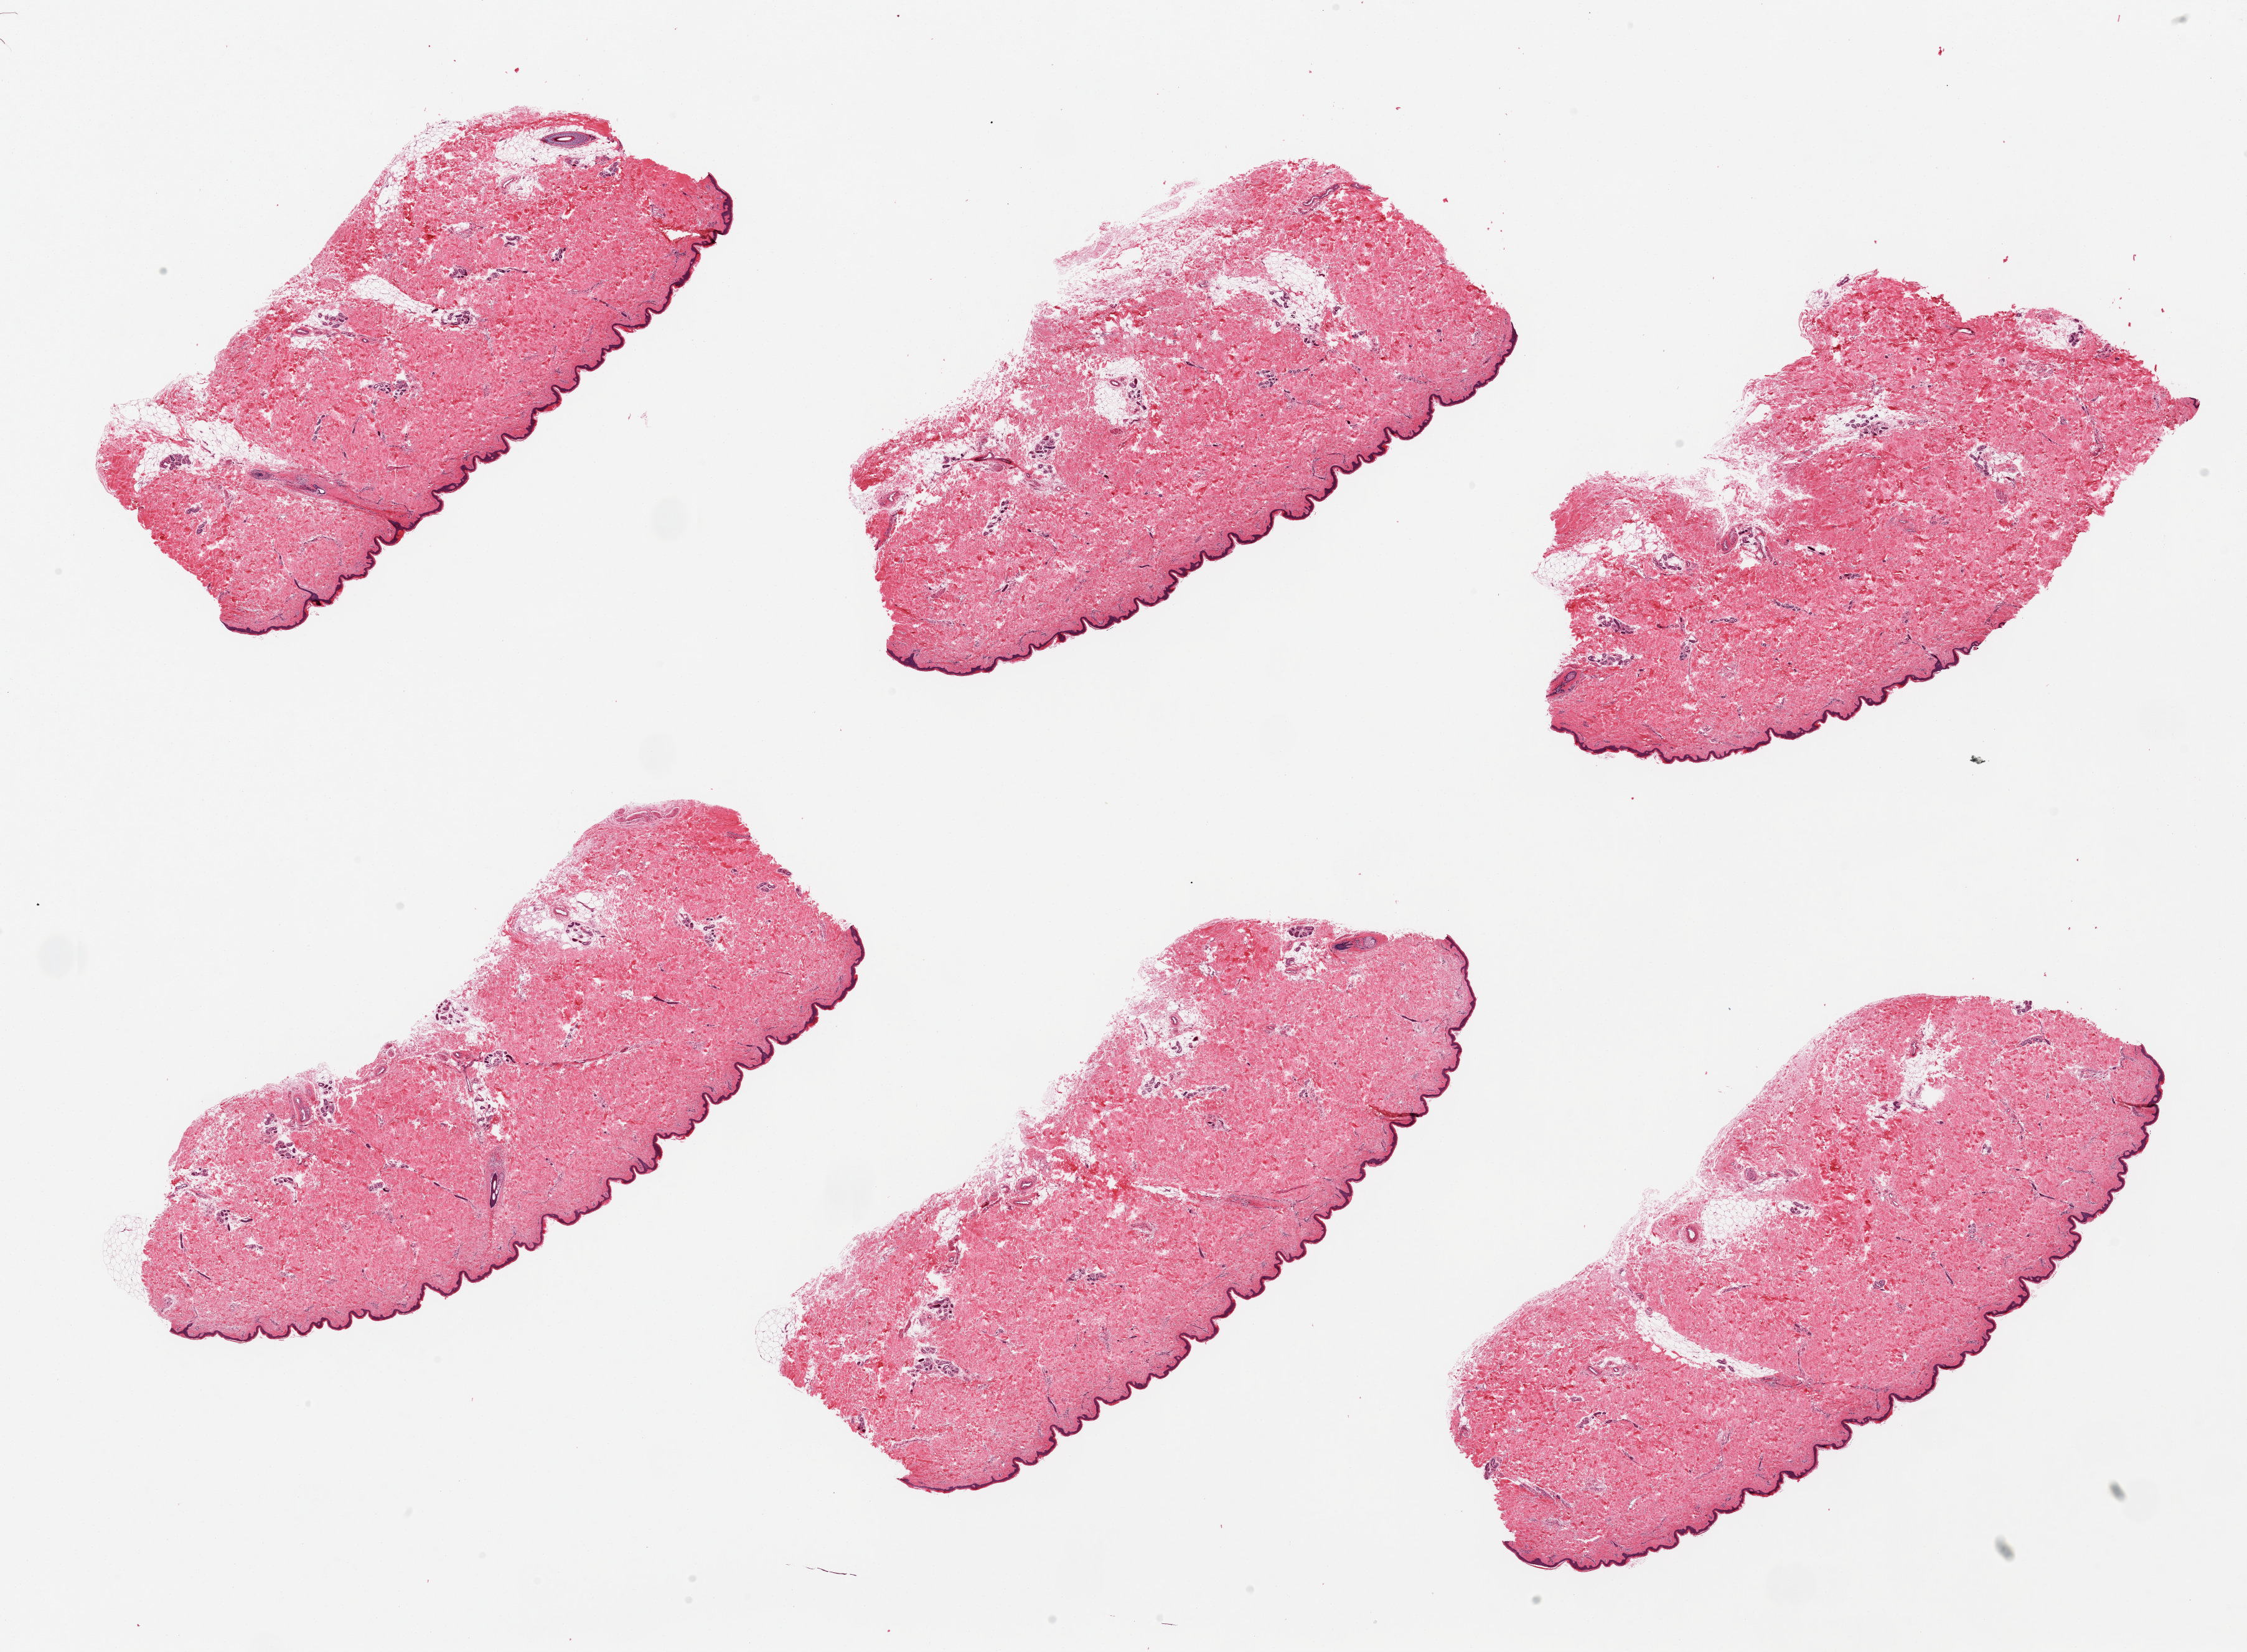
Whole-slide image, hematoxylin and eosin (H&E) stain — whole scanned area (about 28.5 x 21.0 mm, from a 20x scan) shown as a low-resolution overview, PAXgene-fixed paraffin-embedded (PFPE) section, section of skin of lower leg (target tissue), donor tissue sample.
Review note (as recorded): 6 pieces, minimal dermal fat; squamous epithelium is ~50 microns.